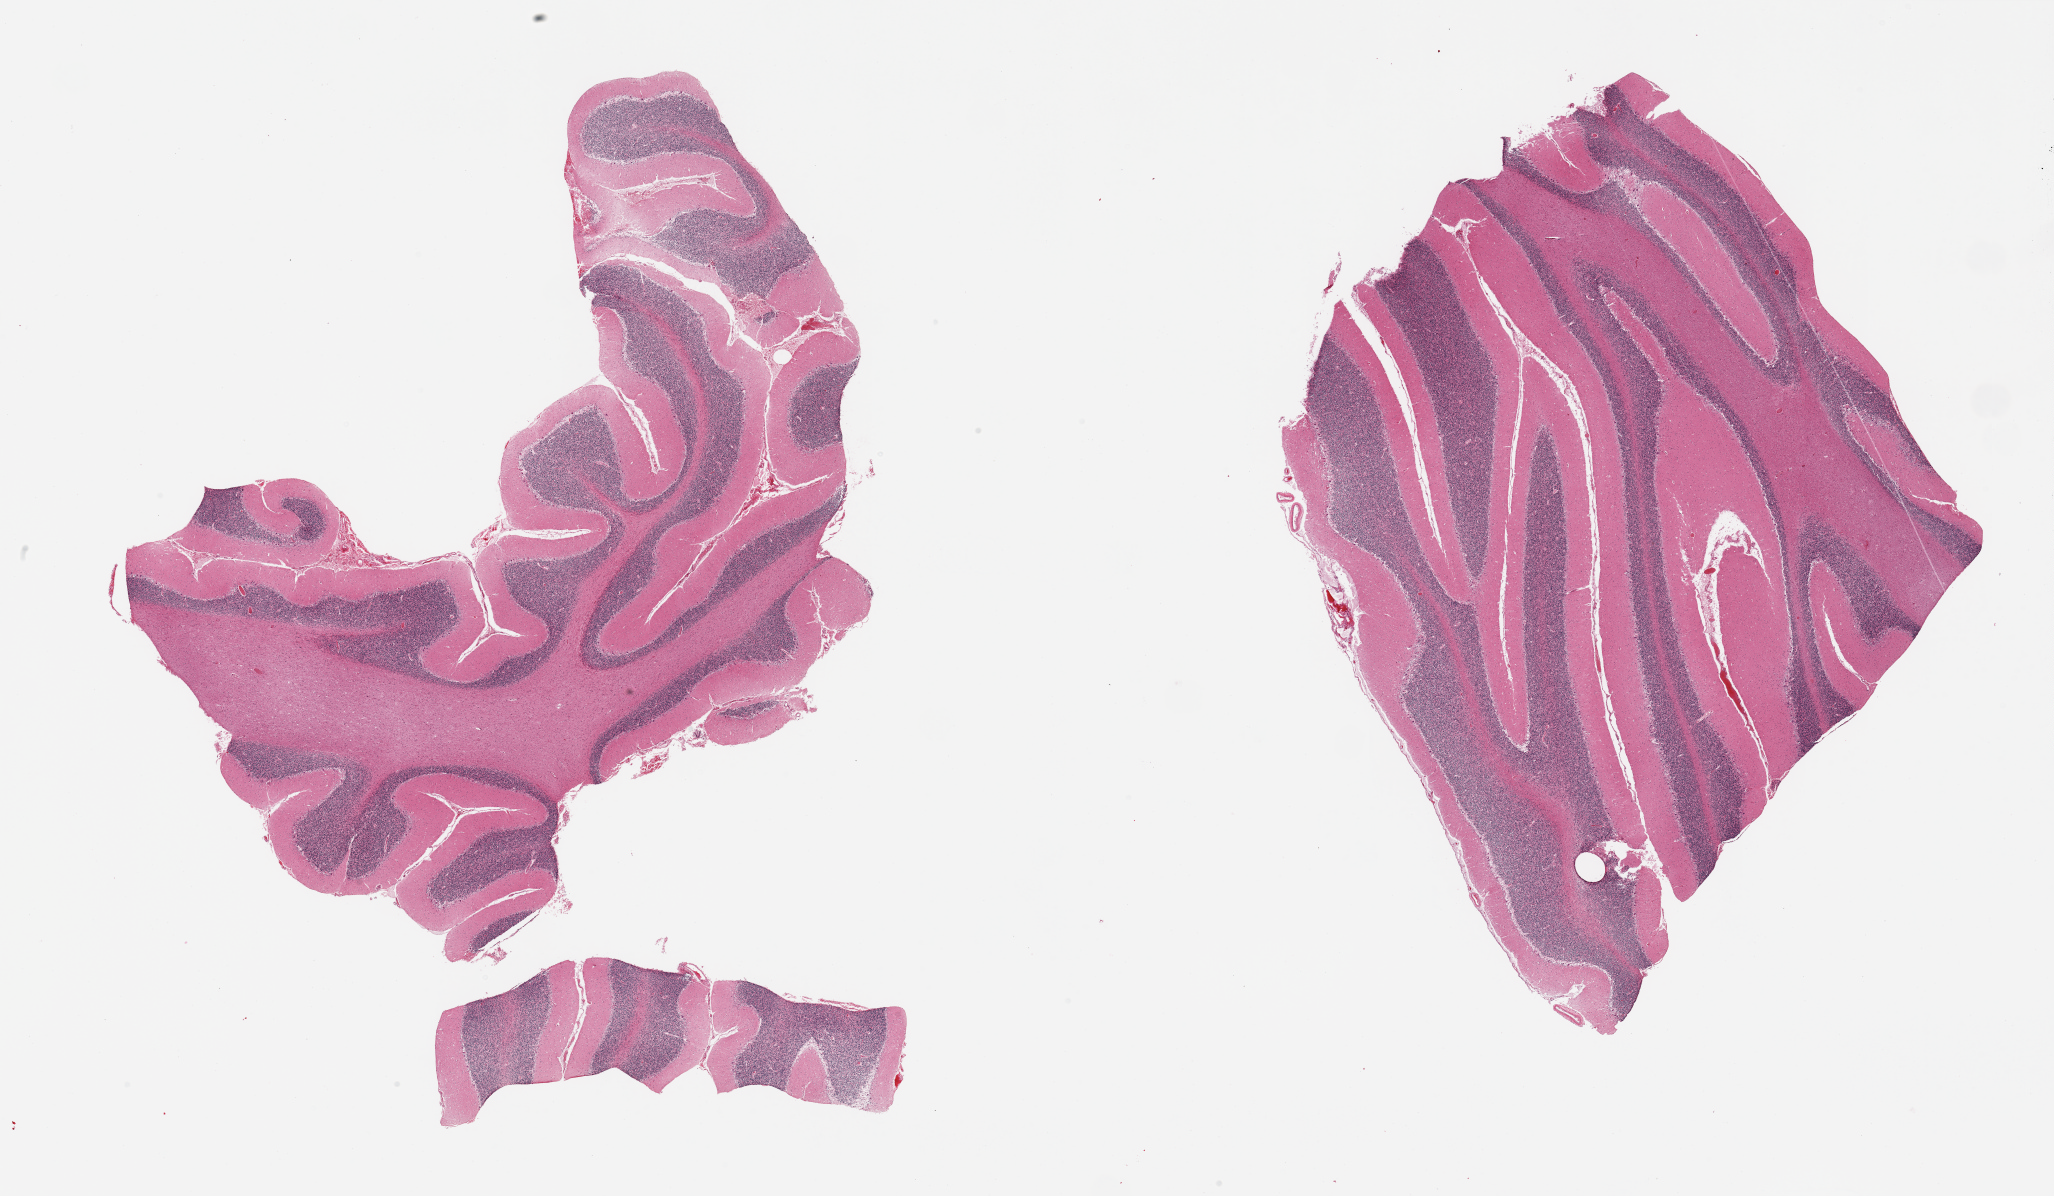
Digitized hematoxylin and eosin (H&E)-stained section — shown as a low-resolution overview of the whole scanned area (about 32.5 x 18.9 mm). PAXgene-fixed paraffin-embedded (PFPE) section. Target tissue: cerebellum. Donor tissue sample. Donor: female.
Review note (as recorded): 2 pieces, no abnormalities.